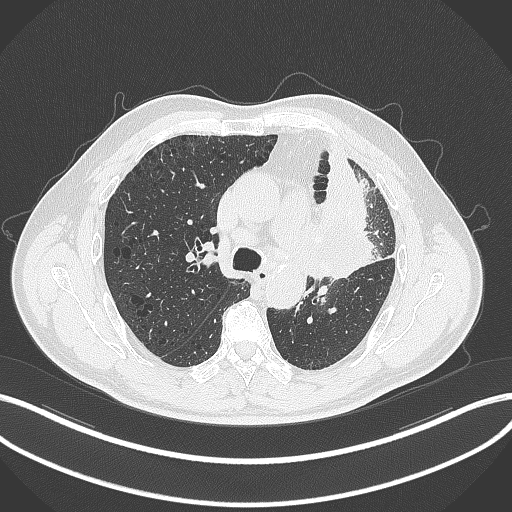
Chest CT, one axial slice. Position 201 of 297 along the scan axis. Reconstruction kernel B70f. Lung window (W 1500 / L -600 HU). 1 mm slice thickness. 512 × 512 image matrix, field of view 400 × 400 mm. Male patient, age 68 years. From the clinical record (not read from this slice): clinical TNM (as recorded): T3 N3 M1.
Annotated regions visible in this slice (bounding box drawn by a radiologist):
- lung tumour (recorded histology: adenocarcinoma): bounding box (x1, y1, x2, y2) in pixels: (302, 196, 380, 281)